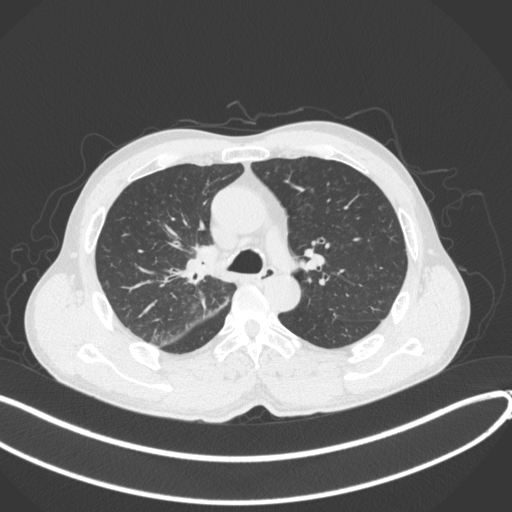
Chest CT, one axial slice; position 259 of 409 along the scan axis; reconstruction kernel B31f; 120 kVp; lung window (W 1500 / L -600 HU); 512 × 512 image matrix, field of view 400 × 400 mm. Male patient, age 53 years. From the clinical record (not read from this slice): clinical TNM (as recorded): T1b N0 M0.
Outlined on this slice (rectangle marked by the reading radiologist):
- lung tumour (recorded histology: squamous cell carcinoma): box from (x=179, y=237) to (x=221, y=289) px